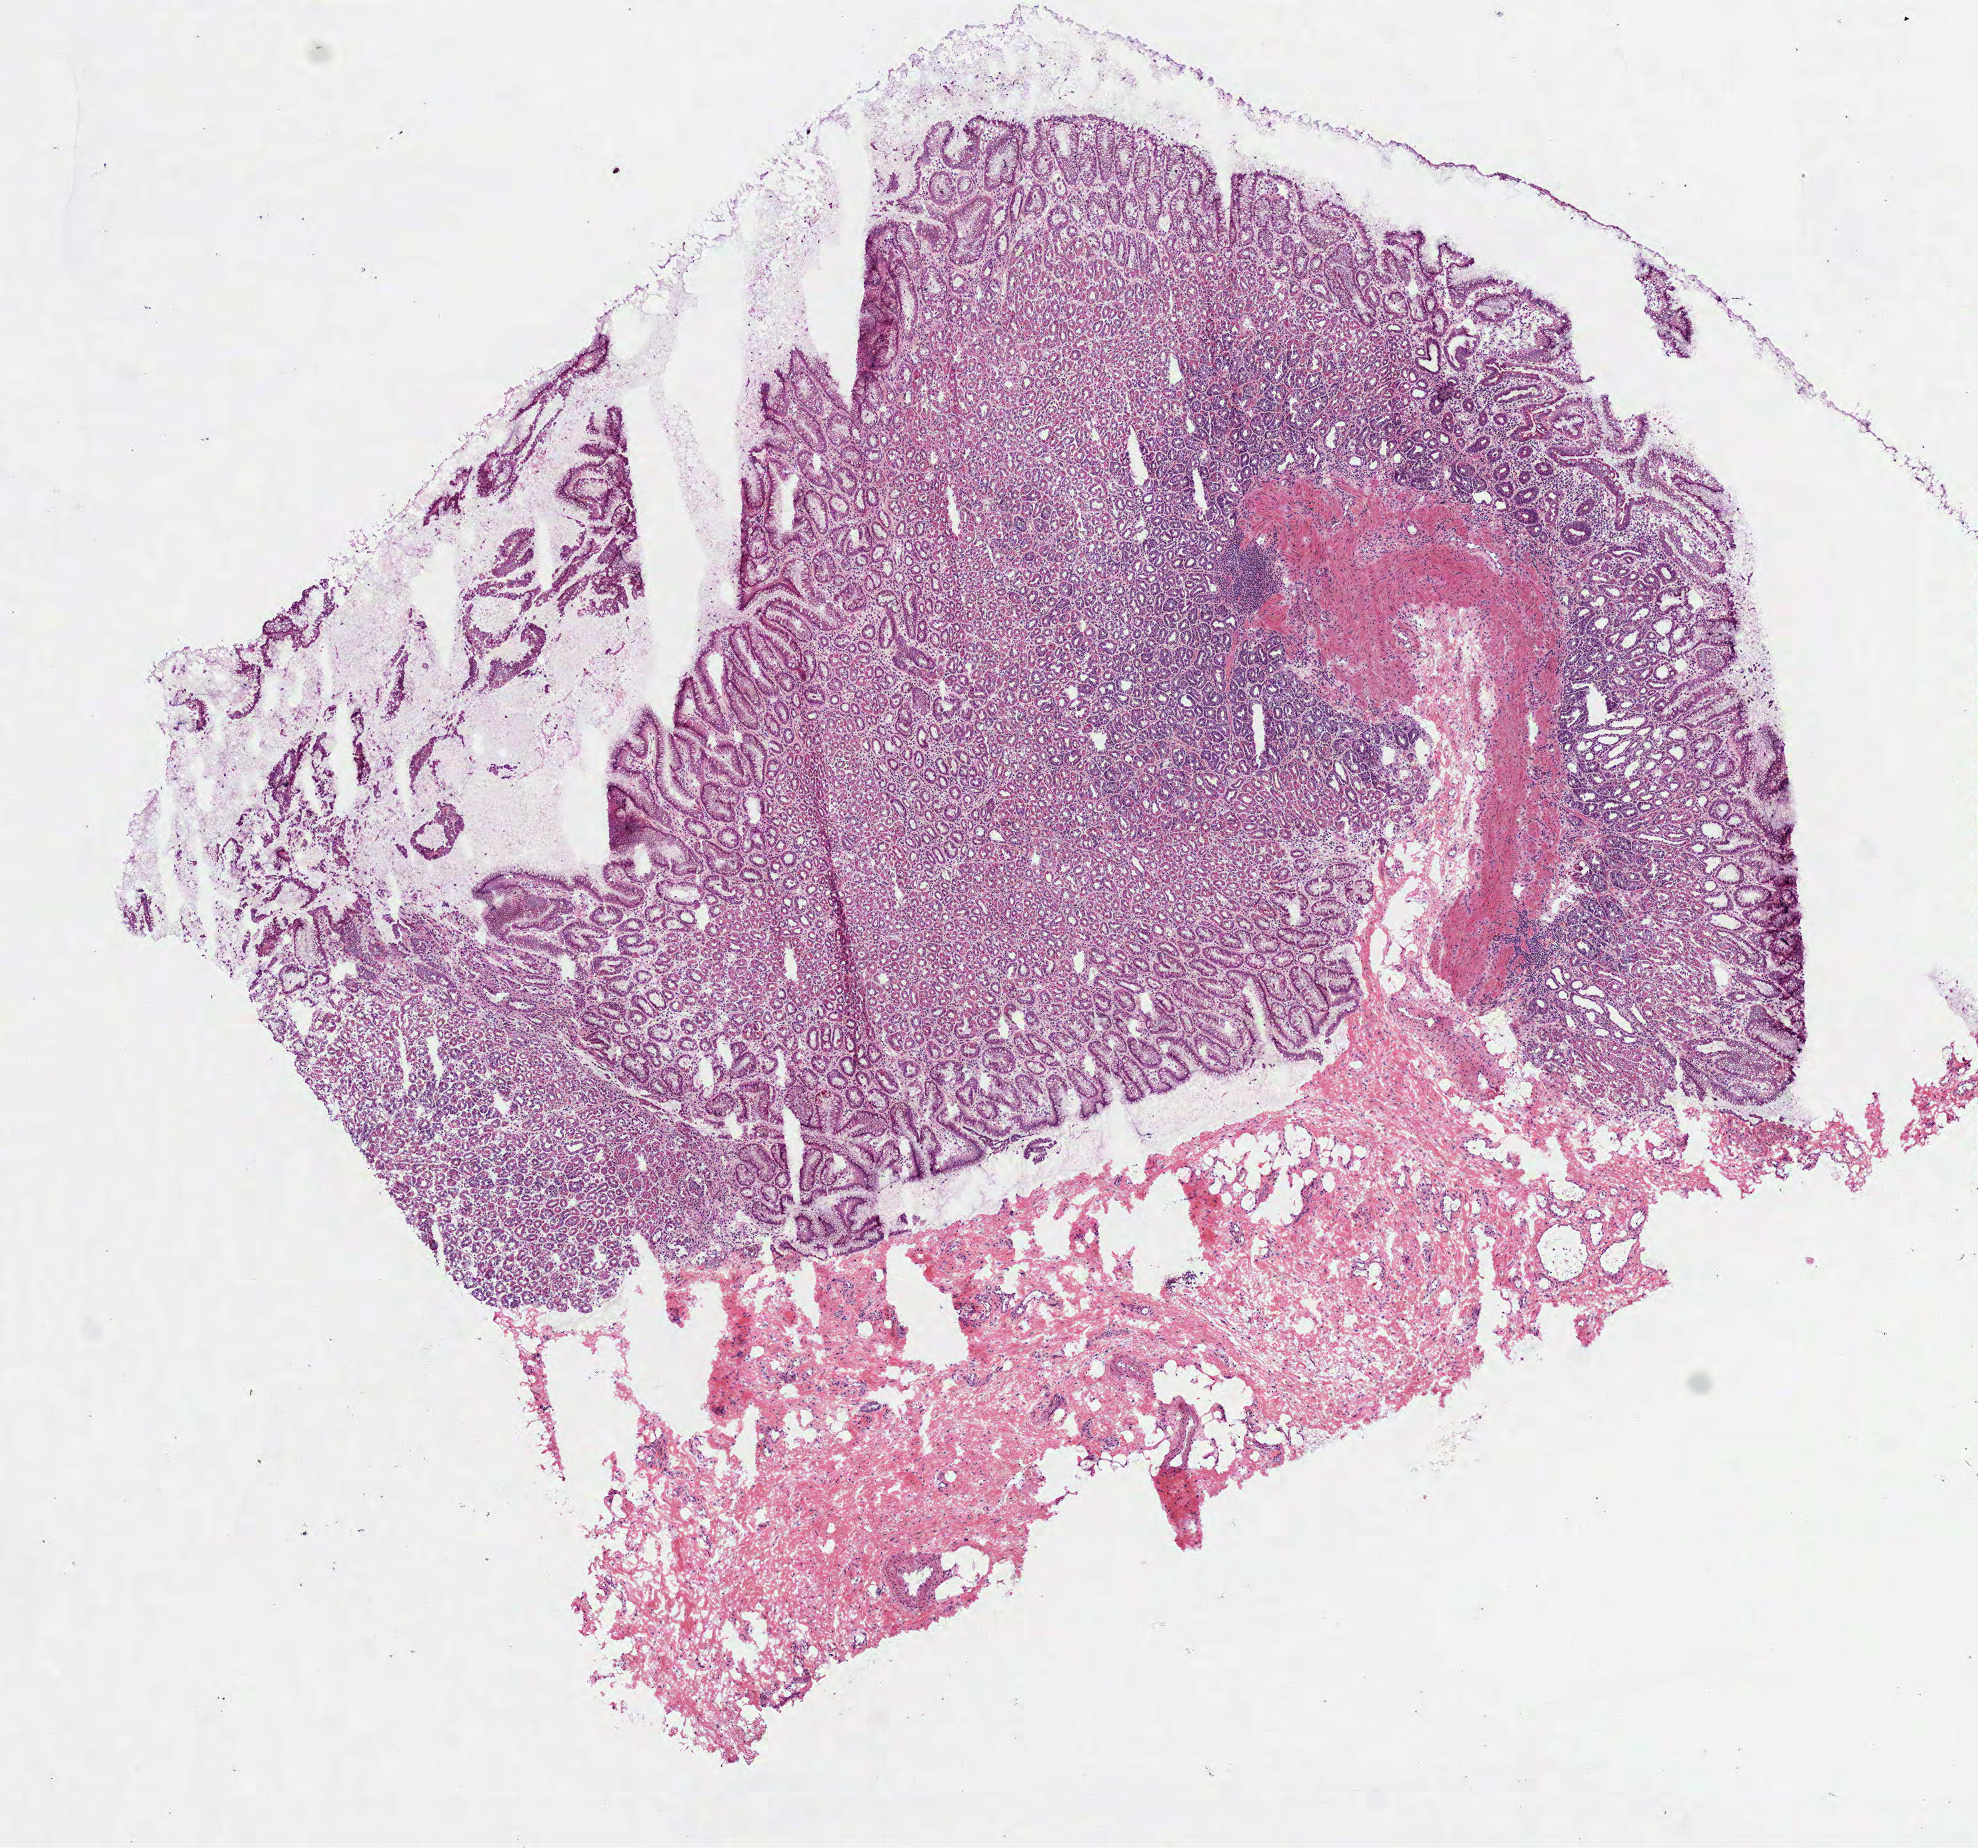
Whole-slide histology image, Hematoxylin and eosin (H&E) stained, shown as a low-resolution overview of the whole scanned area (about 8.0 x 7.5 mm, slide scanned at 40x). Frozen section from the top of the tissue portion. Stomach, solid tissue normal (non-tumour tissue) sample. Male, age 79 years at initial diagnosis.
This section: solid tissue normal (non-tumour) sample from the same patient. Patient diagnosis: Adenocarcinoma, NOS.